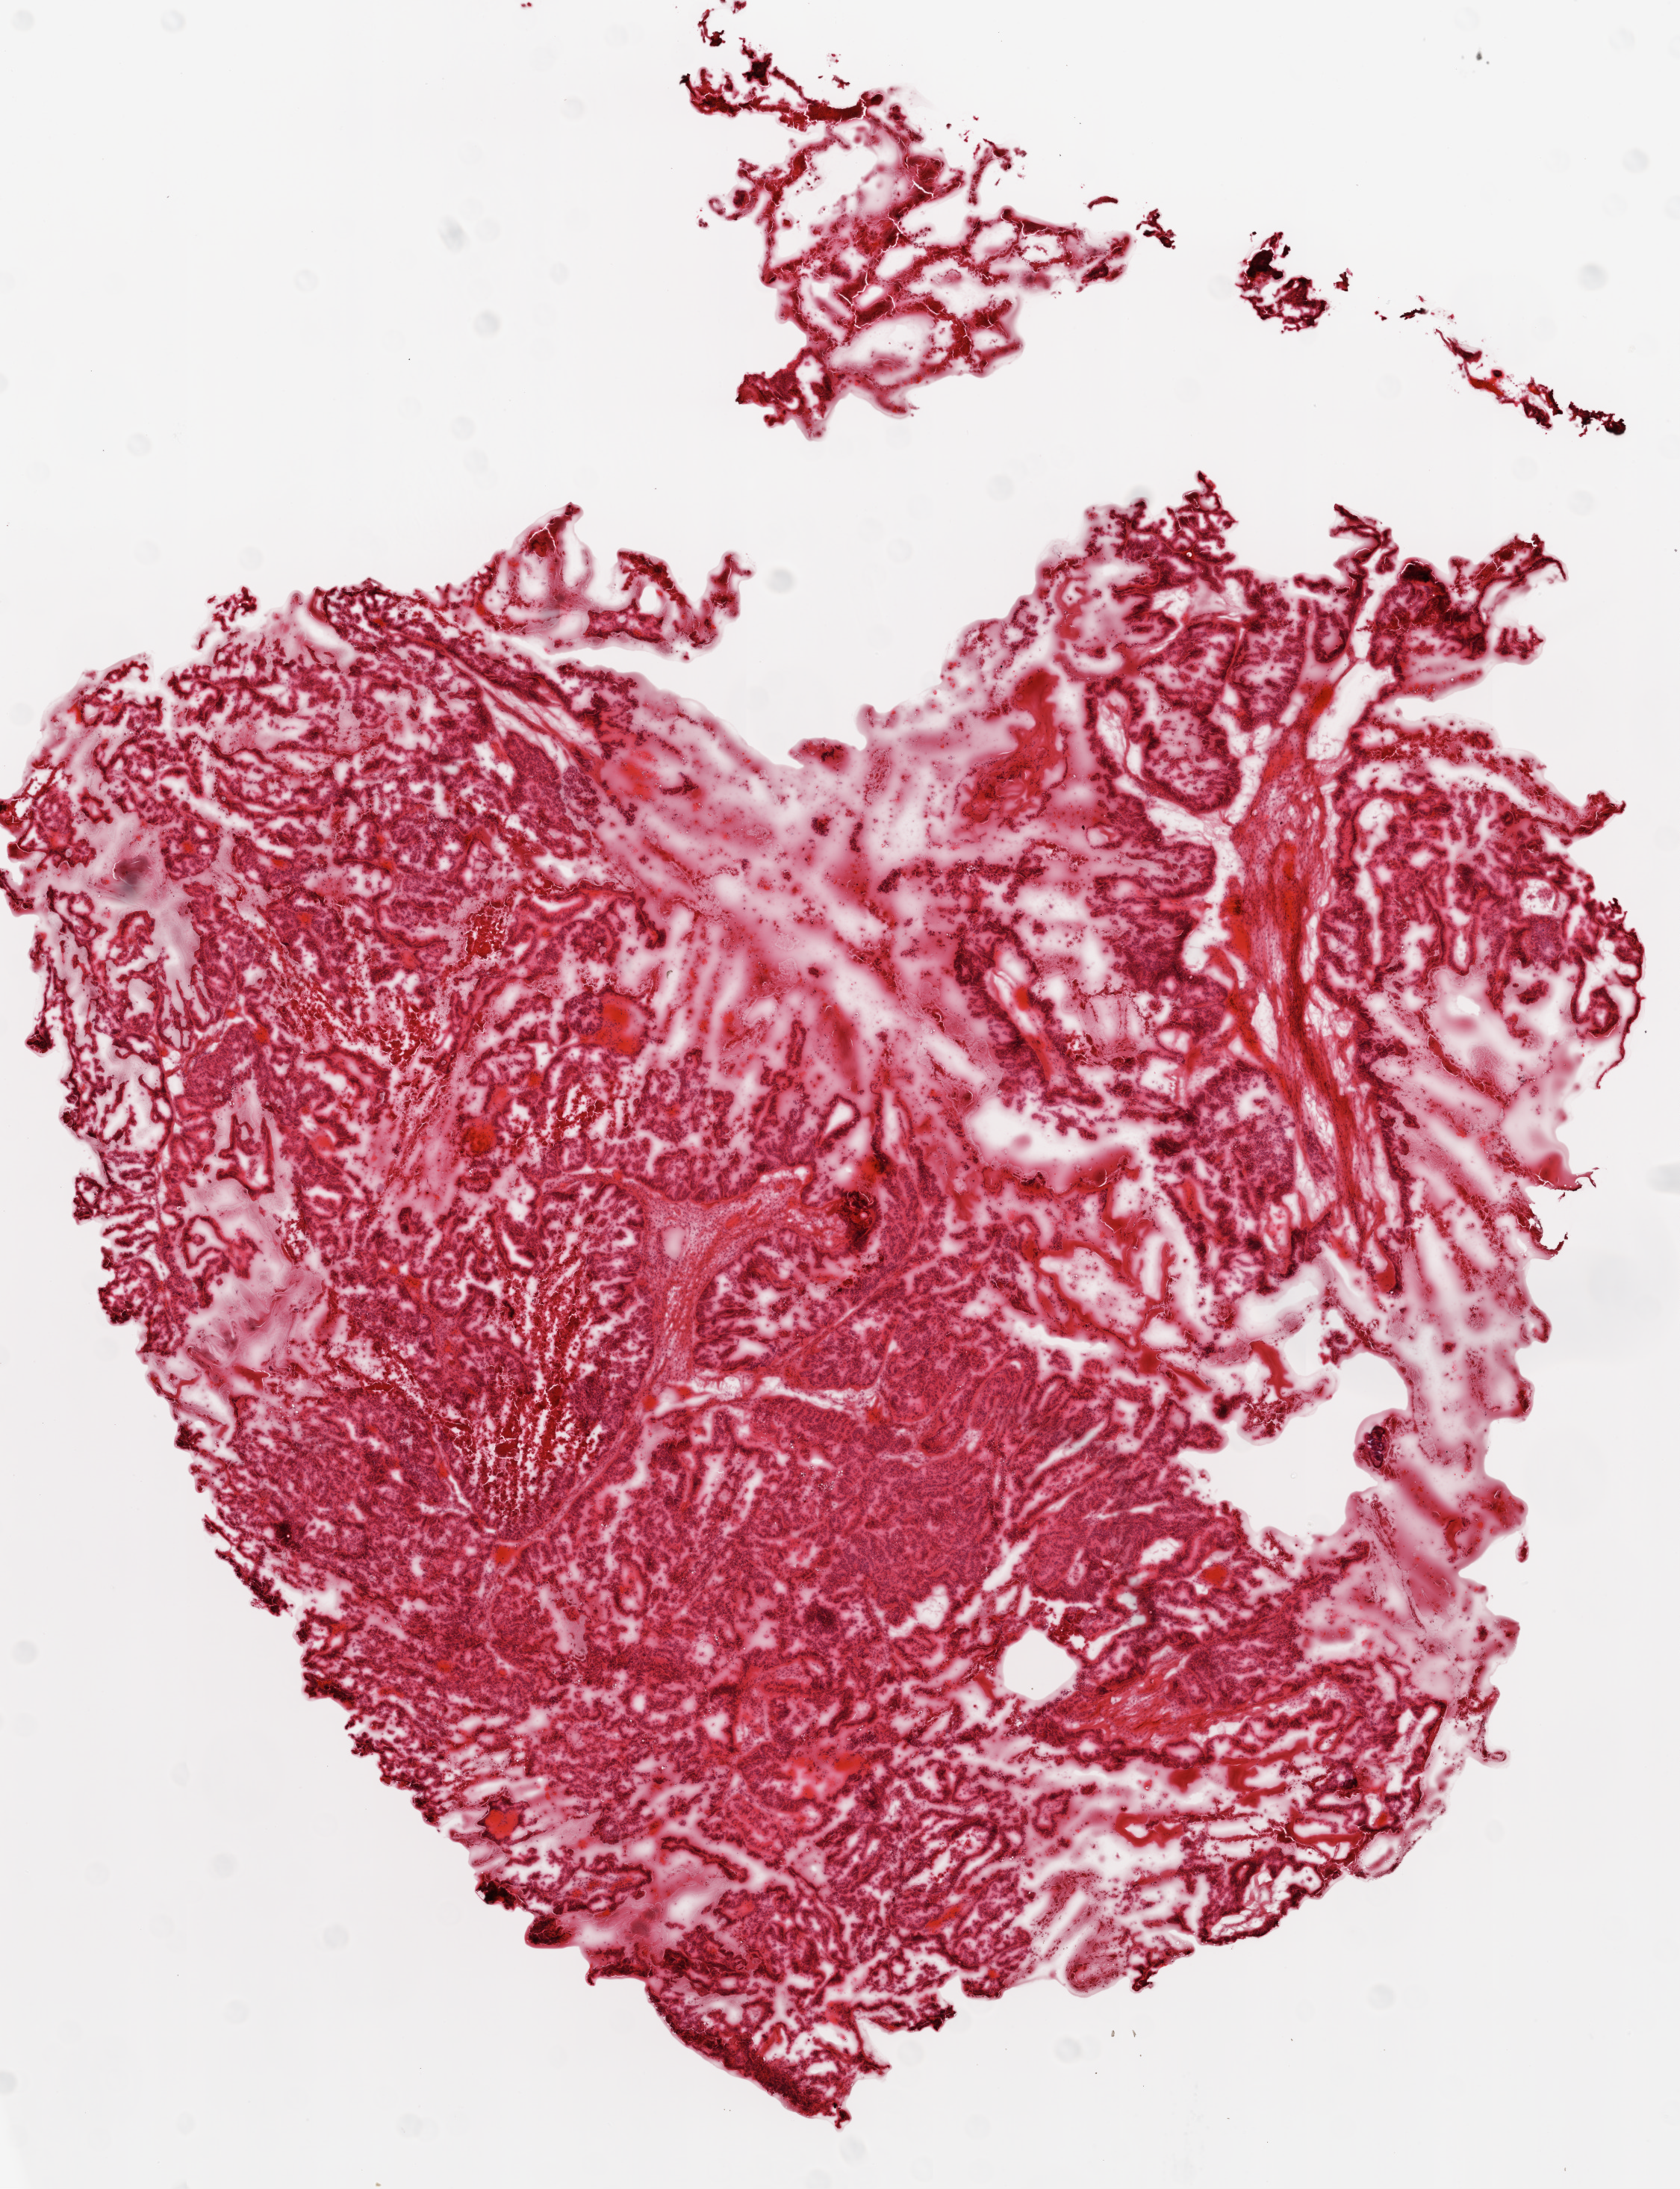
Hematoxylin and eosin (H&E) stained whole-slide image — low-resolution overview of the scanned area, about 9.0 x 11.8 mm; frozen section from the top of the tissue portion; primary tumour sample from the ovary. Patient: female, age at initial diagnosis 71 years. Histologic grade: G3 (poorly differentiated). Composition of this section per pathologist review: tumour cells 75%, tumour nuclei 80%, normal cells 0%, stromal cells 20%, necrosis 5%.
Laterality: bilateral. FIGO stage: IIIC. Diagnosis: Serous cystadenocarcinoma, NOS.